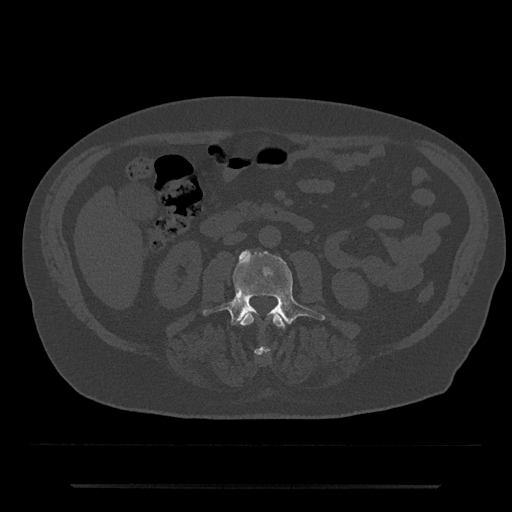
CT including the spine, one axial slice. Position 425 of 797 along the scan axis. Reconstruction kernel Br40s/3. 120 kVp. Bone window (W 1800 / L 400 HU). 0.5 mm slice thickness. 512 × 512 image matrix. Patient: male, 80 years. Case-level facts recorded for this patient, not image findings: primary cancer: prostate; vertebrae with lytic lesions (as recorded): L1, T11.
Structures marked on this image (semi-automatically segmented with operator editing):
- L2 vertebra: bounding box <240,311,285,355> (left, top, right, bottom; pixels)
- L3 vertebra: <203,250,325,325>